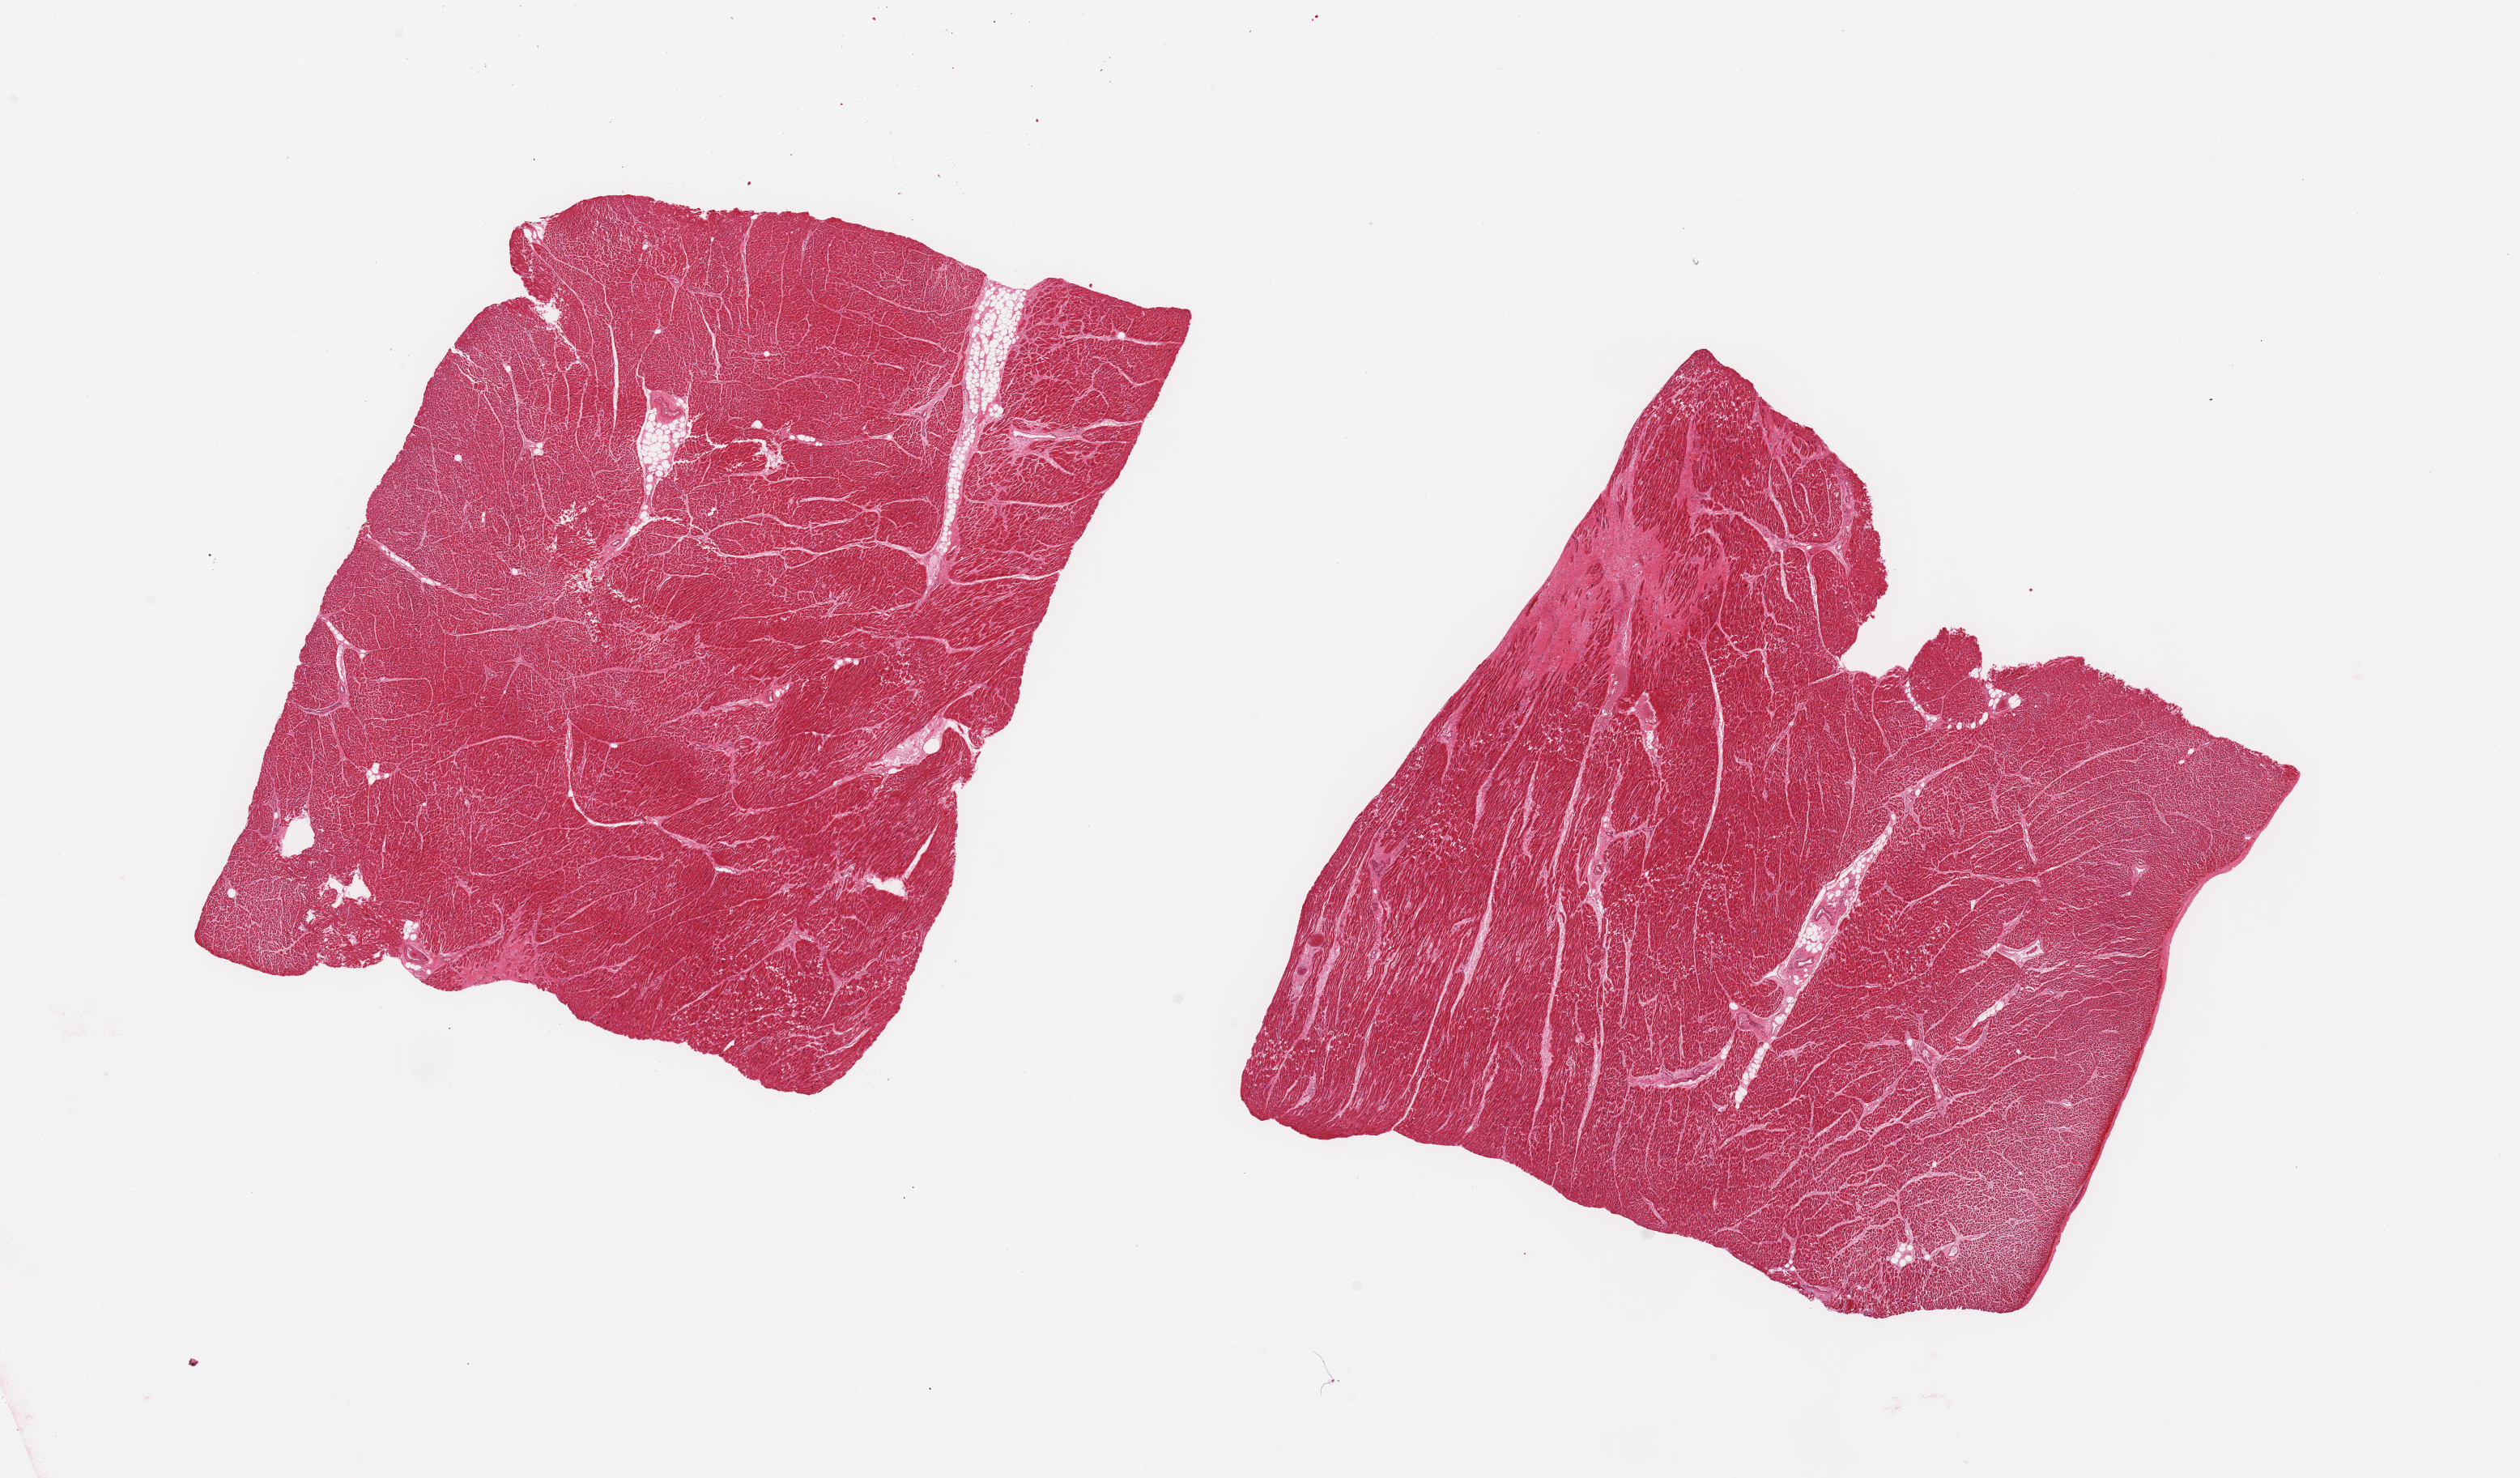
Digitized H&E-stained section, brightfield — a low-resolution overview of the entire scanned area, about 24.6 x 14.4 mm (from a 20x scan). PAXgene-fixed, paraffin-embedded tissue. Sampled site (target tissue): heart. Tissue donor sample. Donor: male.
Pathologist's review note for this sample: 2 pieces; patchy areas of scar, some fragmentation of fibers, small component of perivascular fat.